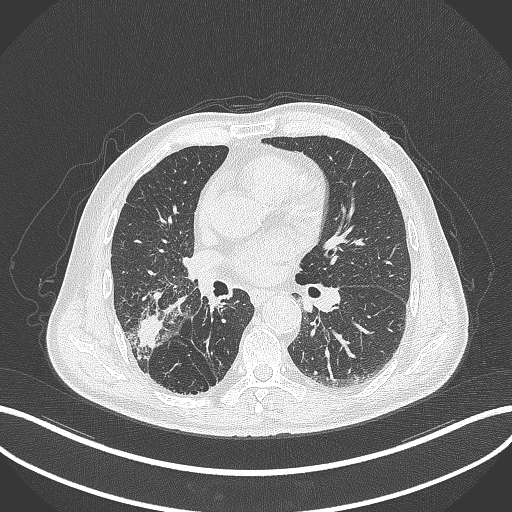
Chest CT, one axial slice; position 212 of 429 along the scan axis; reconstruction kernel B70f; 120 kVp; lung window (W 1500 / L -600 HU); 1 mm slice thickness; 512 × 512 image matrix, field of view 400 × 400 mm. Male patient, age 72 years. From the clinical record (not read from this slice): clinical TNM (as recorded): T3 N2 M0.
Annotated regions visible in this slice (rectangle marked by the reading radiologist):
- lung tumour (recorded histology: adenocarcinoma): bounding box [x1, y1, x2, y2] px = [133, 313, 165, 353]